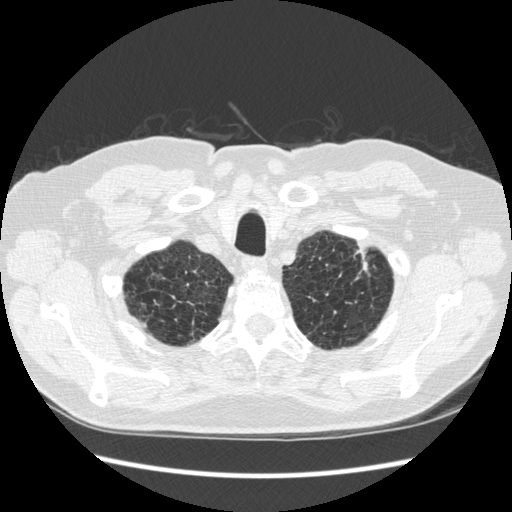
Low-dose screening chest CT, one axial slice. Slice 240 of 267 in the series (ordered by position). Reconstruction kernel STANDARD. 120 kVp. Lung window (W 1500 / L -600 HU). 1.25 mm slice thickness. 512 × 512 image matrix.
Outlined on this slice (outlined manually by an expert reader):
- lesion 1 (tumor, upper lobe of left lung): box from (x=356, y=252) to (x=368, y=271) px